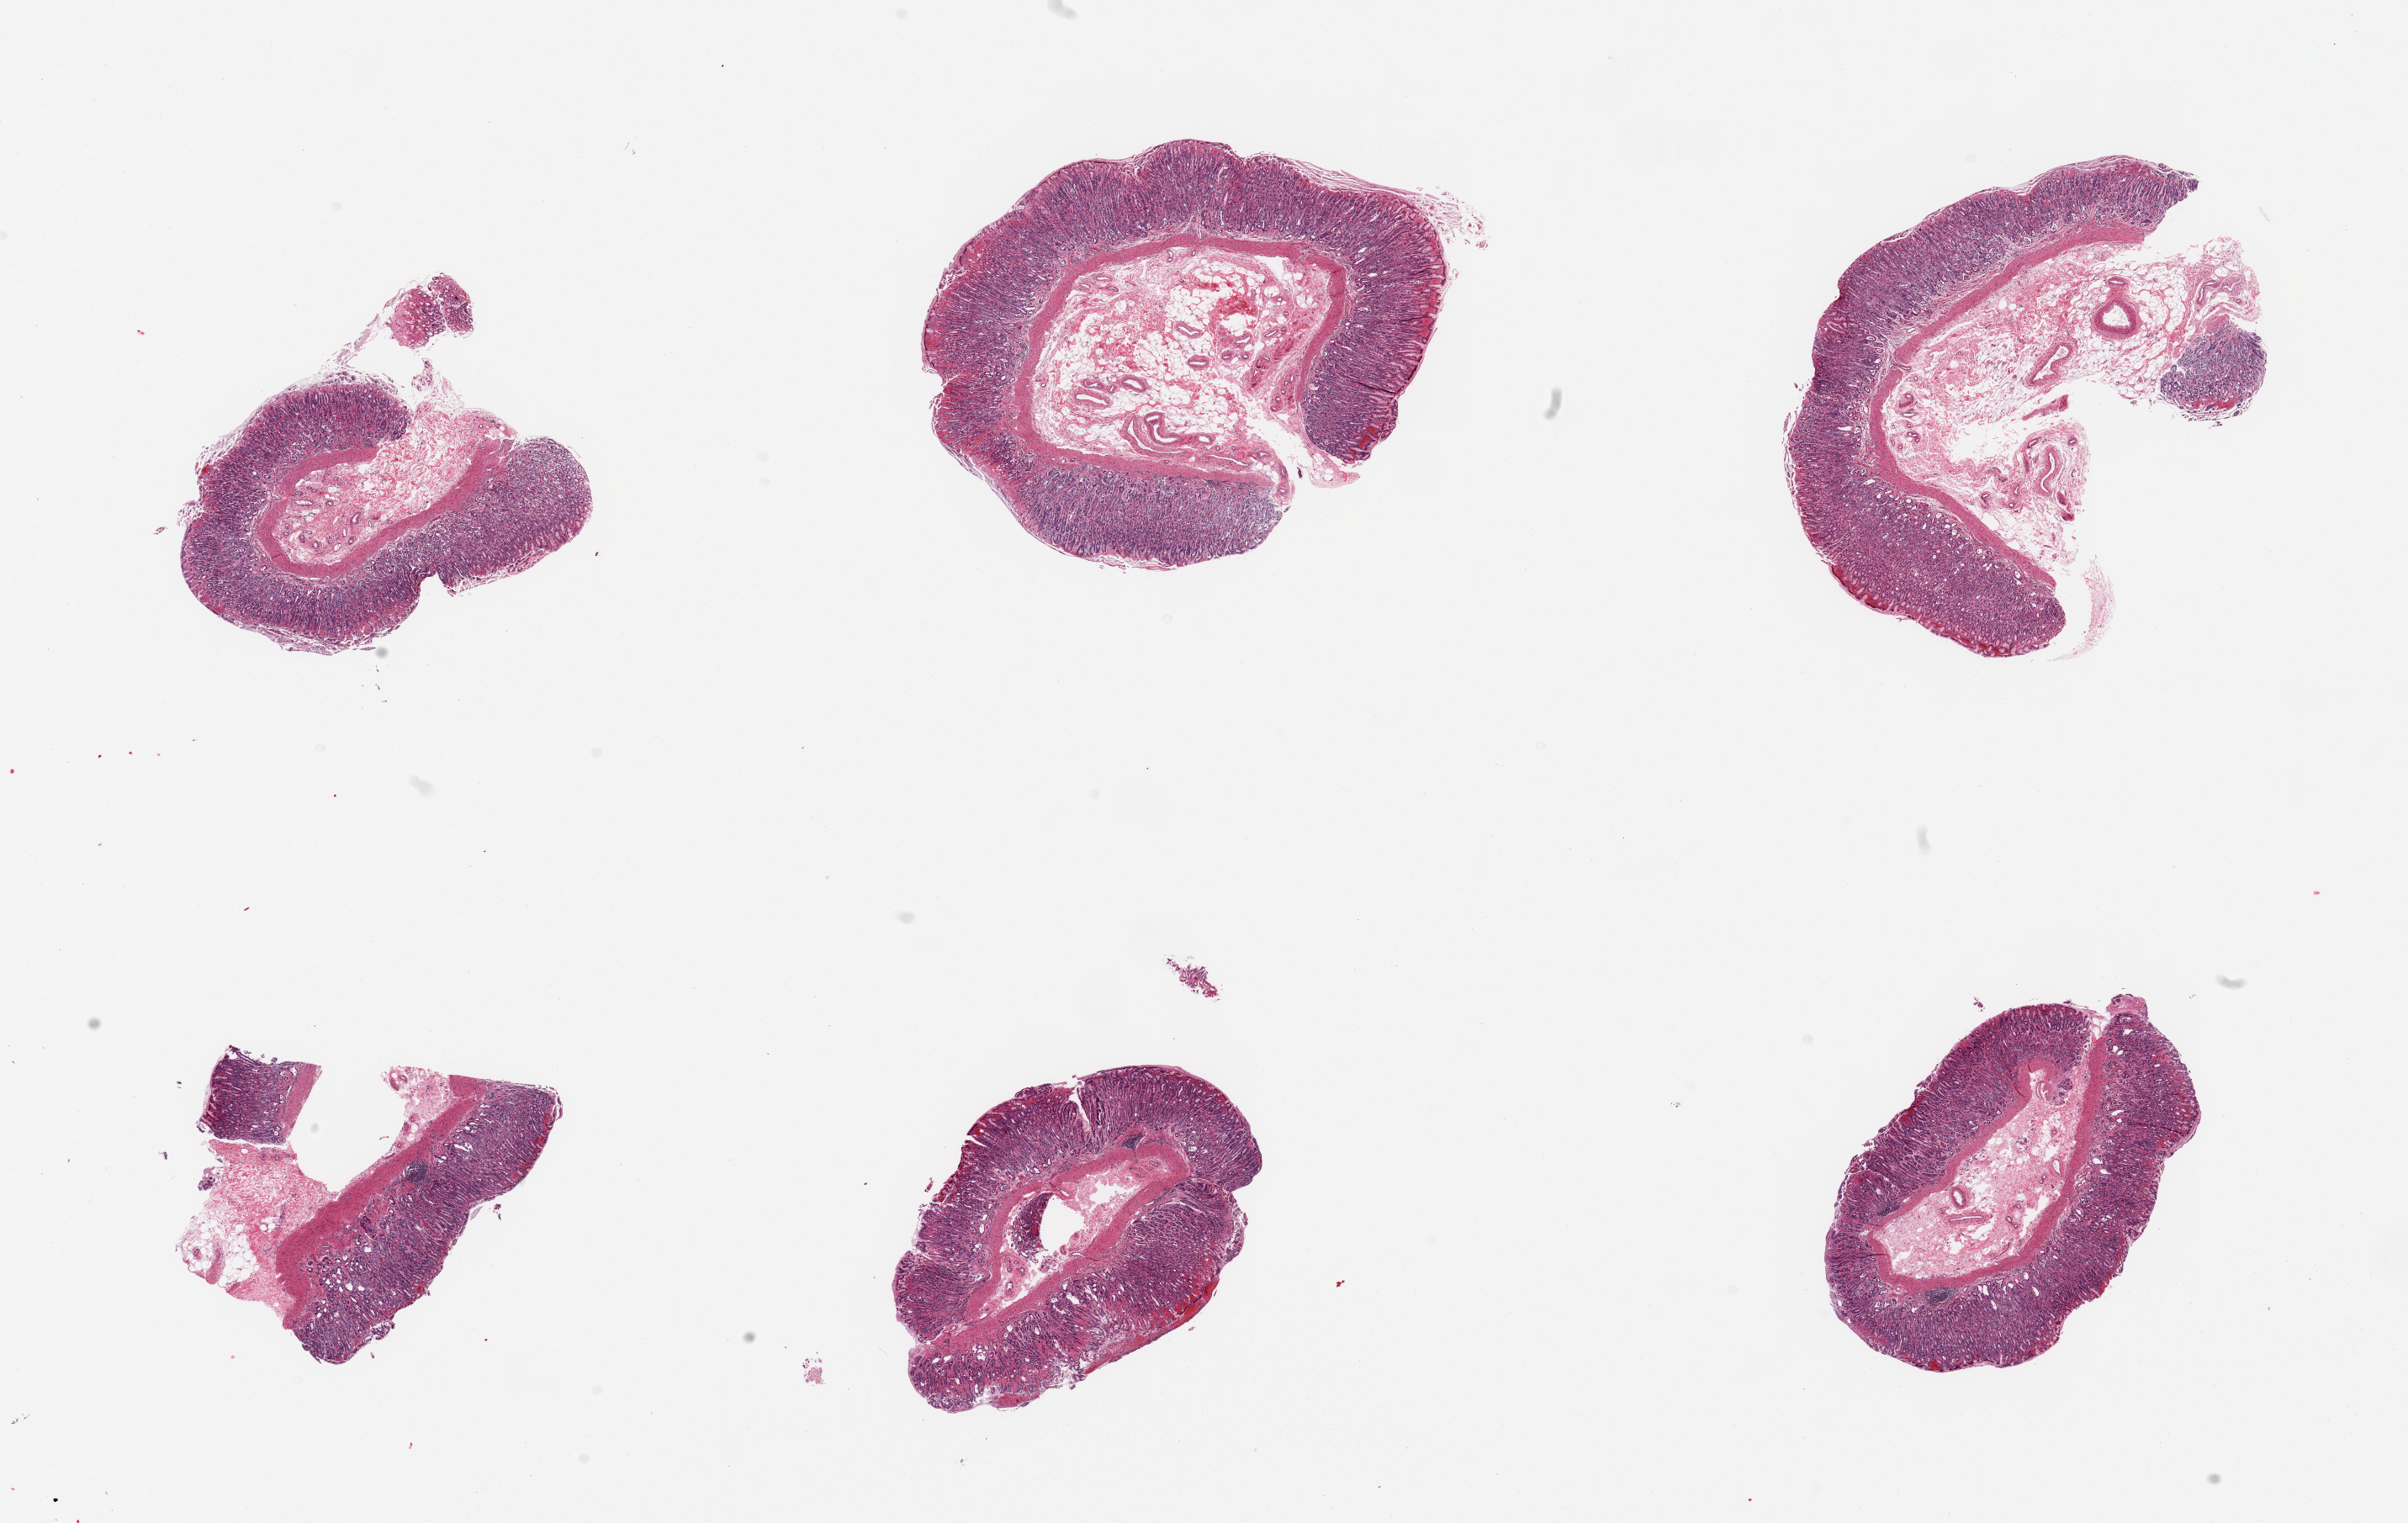
Digitized haematoxylin and eosin-stained section, shown as a low-resolution overview of the whole scanned area (about 22.6 x 14.3 mm, slide scanned at 20x). PAXgene-fixed paraffin-embedded (PFPE) section. Section of stomach (target tissue). Donor tissue sample. Male donor.
• pathologist's review note for this sample: 6 pieces; gastric mucosa but no muscularis; fresh hemorrhage in the lamina propria of the superficial part of mucosa; microcystic deep glandular changes